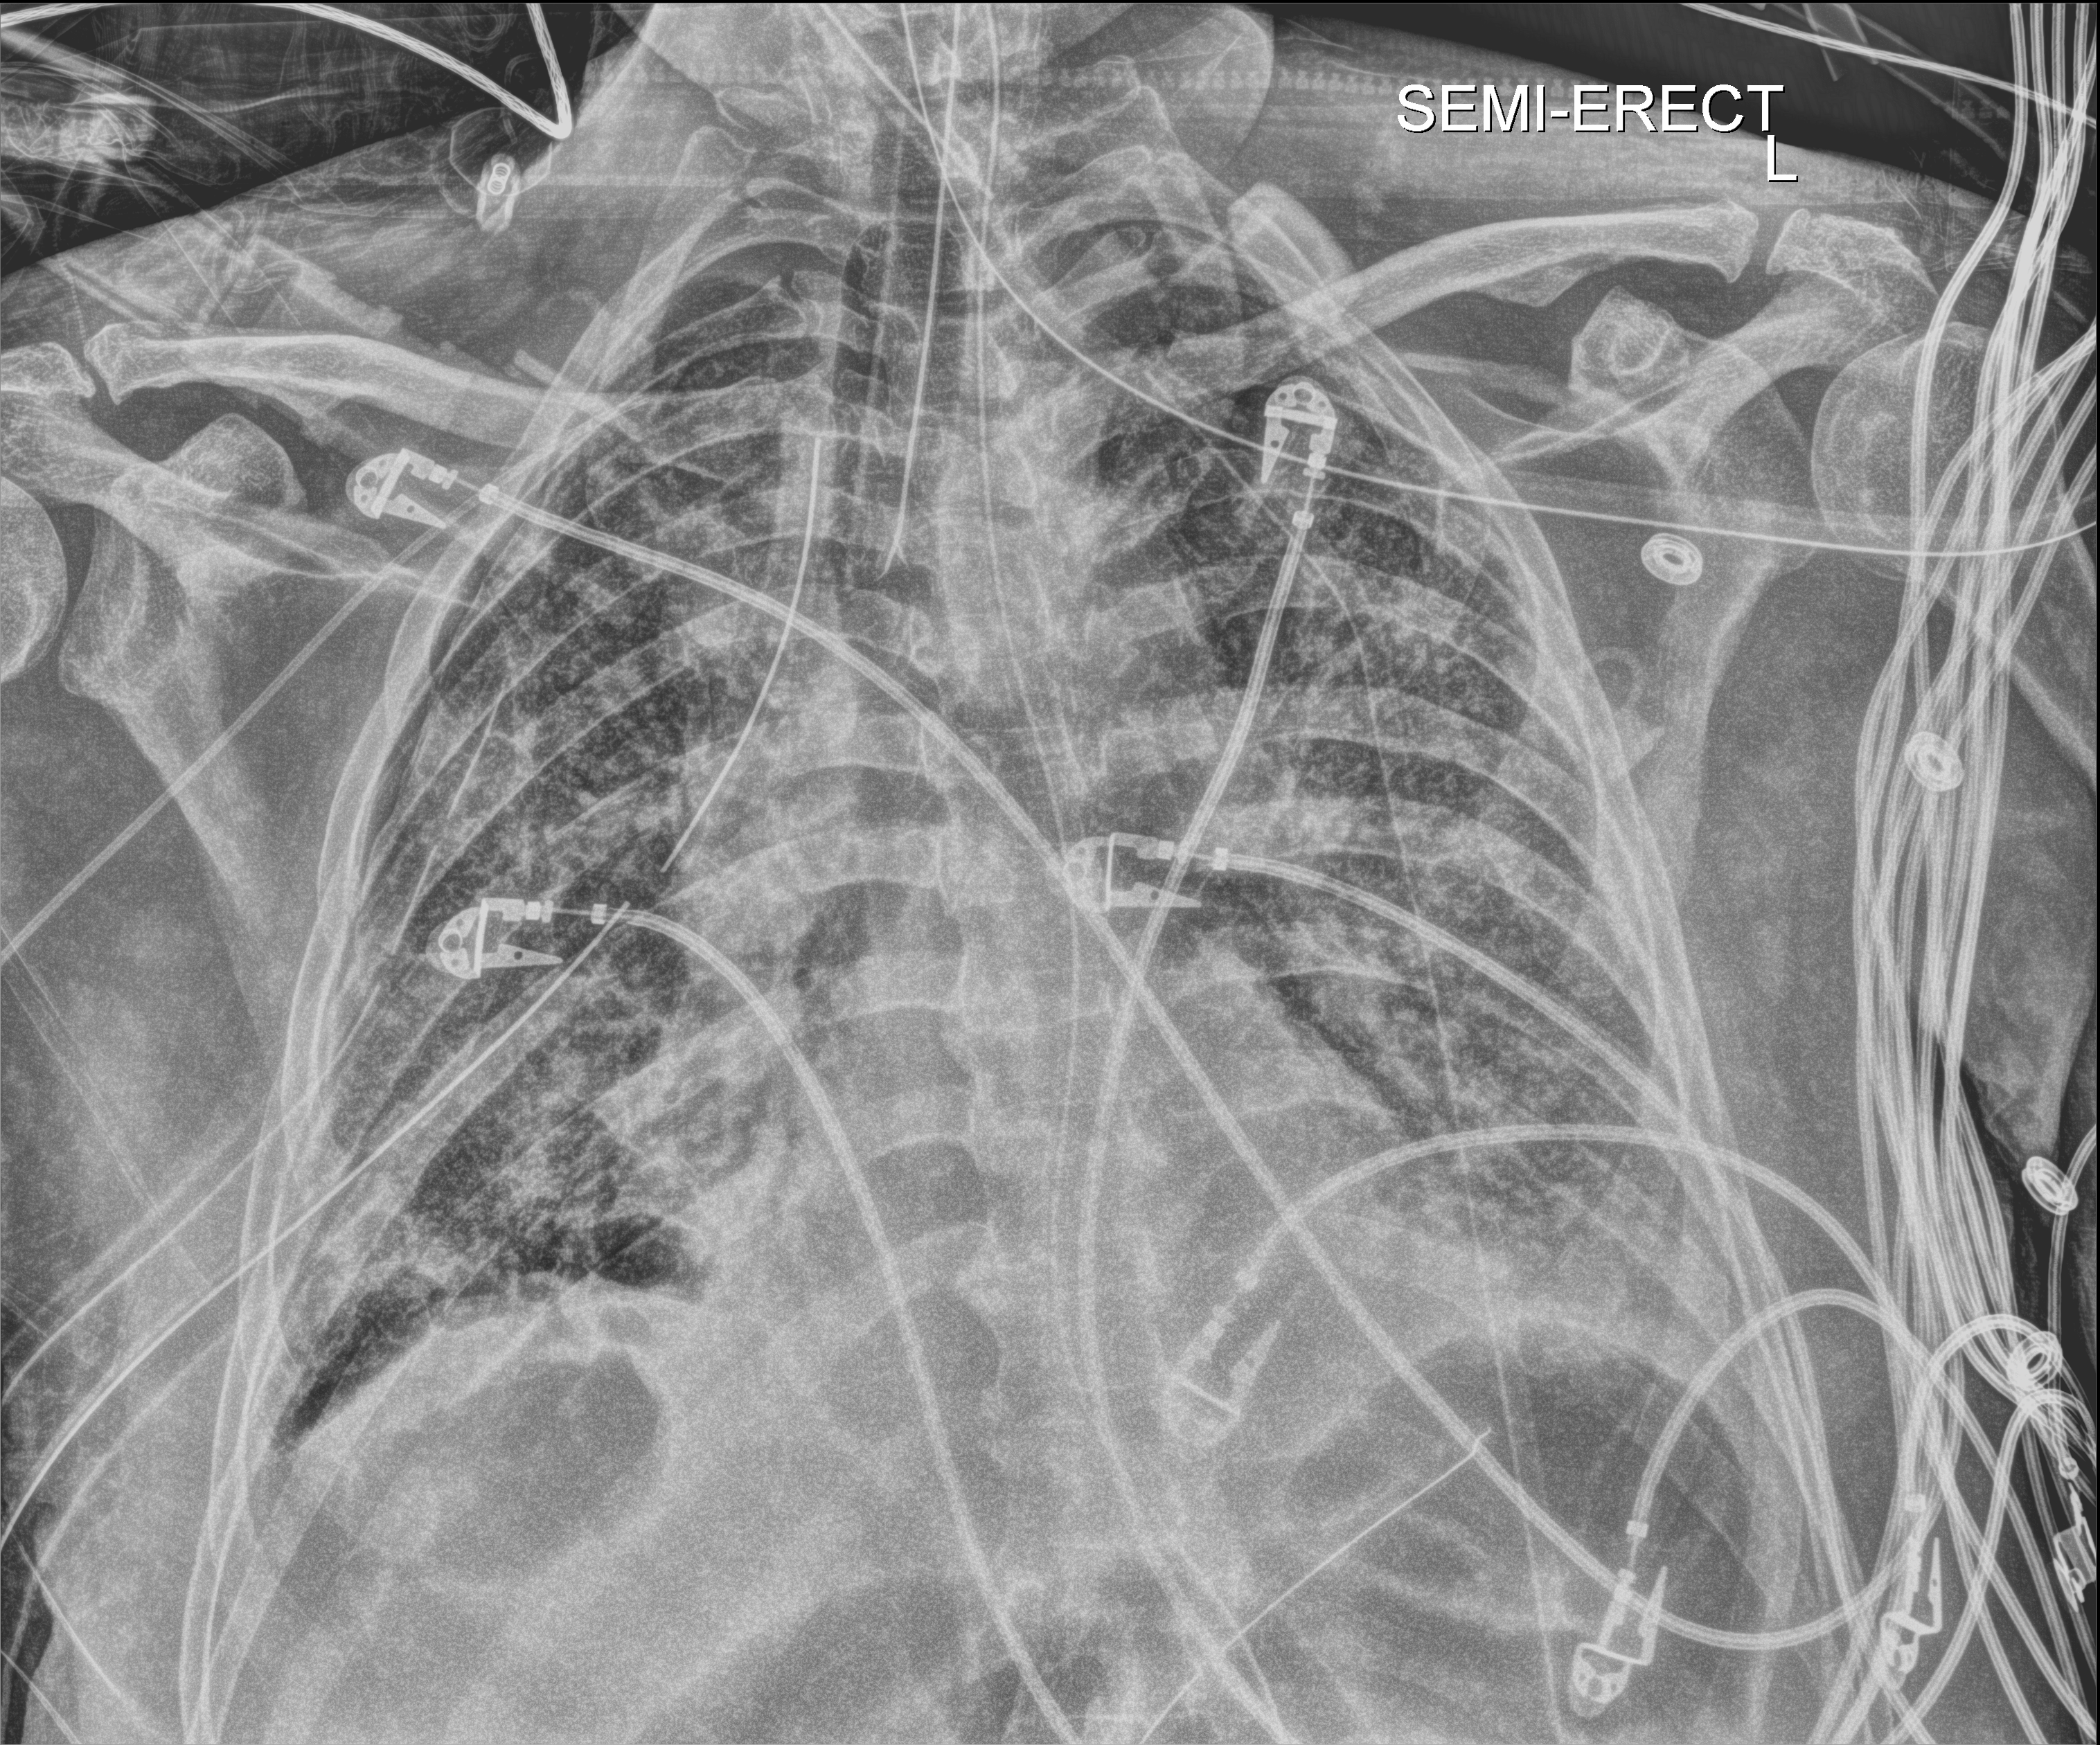
Chest radiograph (digital radiography). Male patient hospitalised with COVID-19, age 60–74 years.
Admission-level facts for this patient (not findings on this image; timing relative to this image not recorded):
- mechanically ventilated during this hospital stay: yes
- admitted to intensive care during this hospital stay: yes